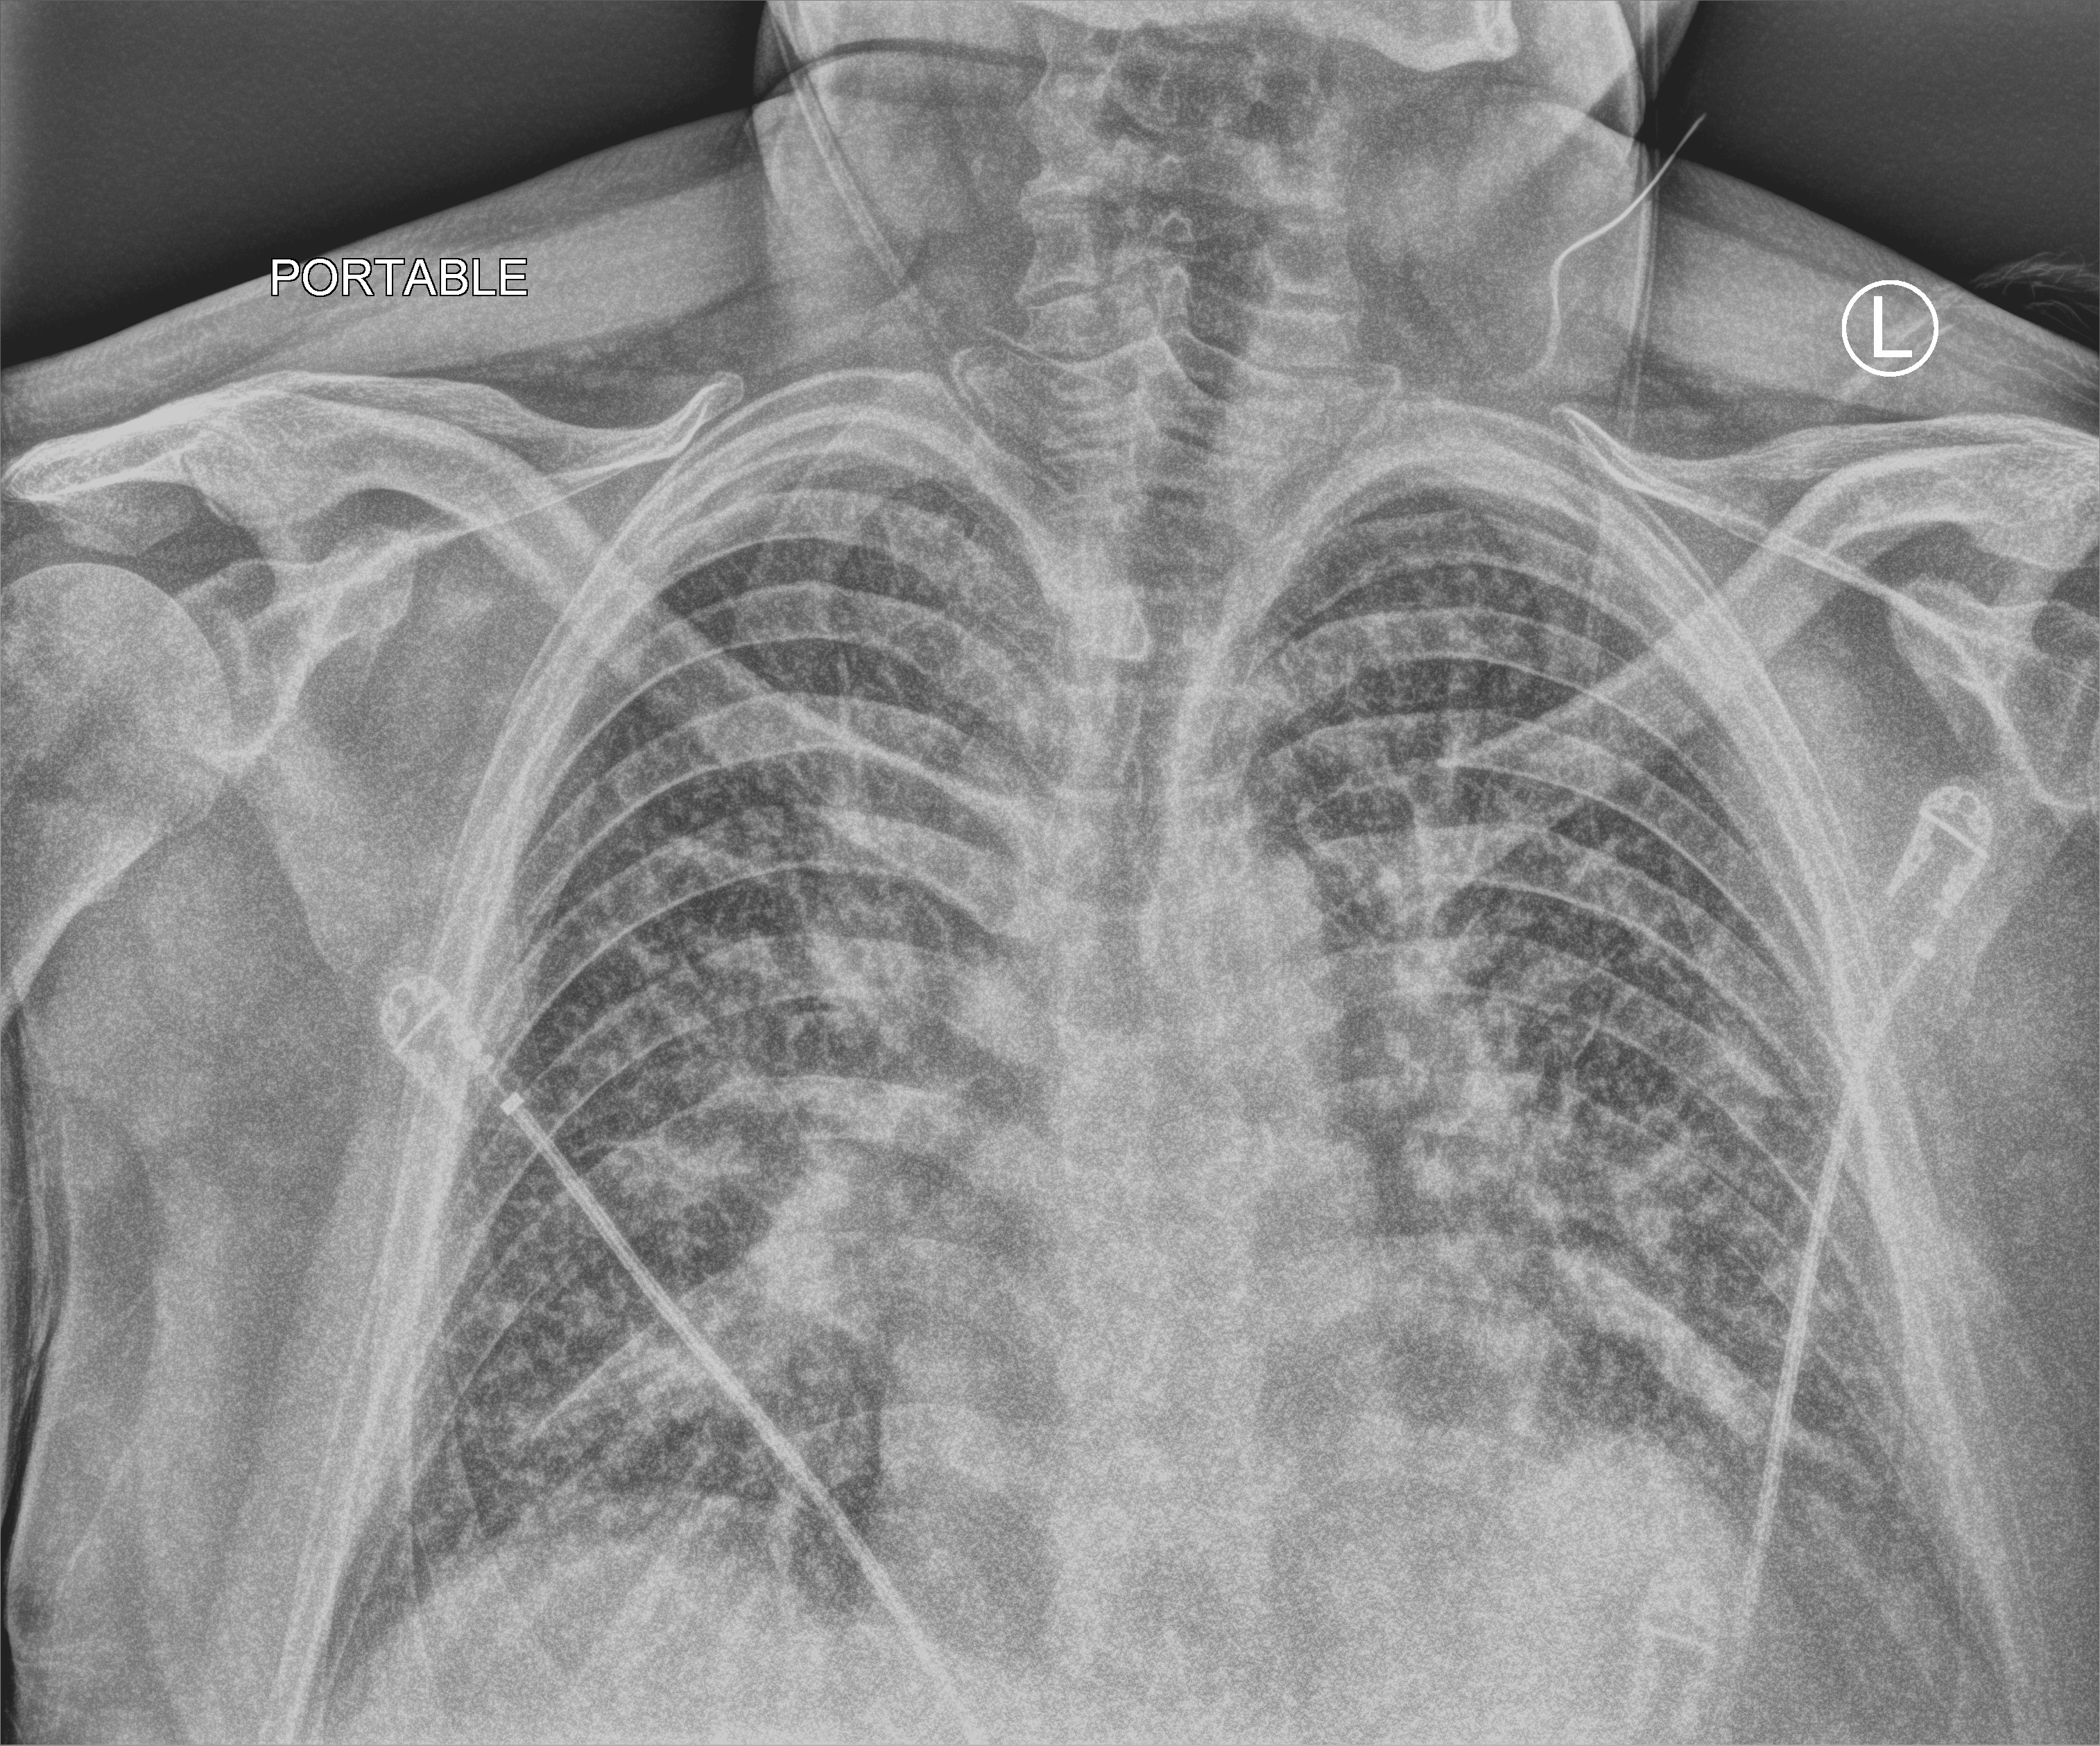
Chest X-ray (portable). Patient hospitalised with COVID-19; male, aged 18–59 years.
Admission-level facts for this patient (not findings on this image; timing relative to this image not recorded): admitted to intensive care during this hospital stay: no; mechanically ventilated during this hospital stay: no.